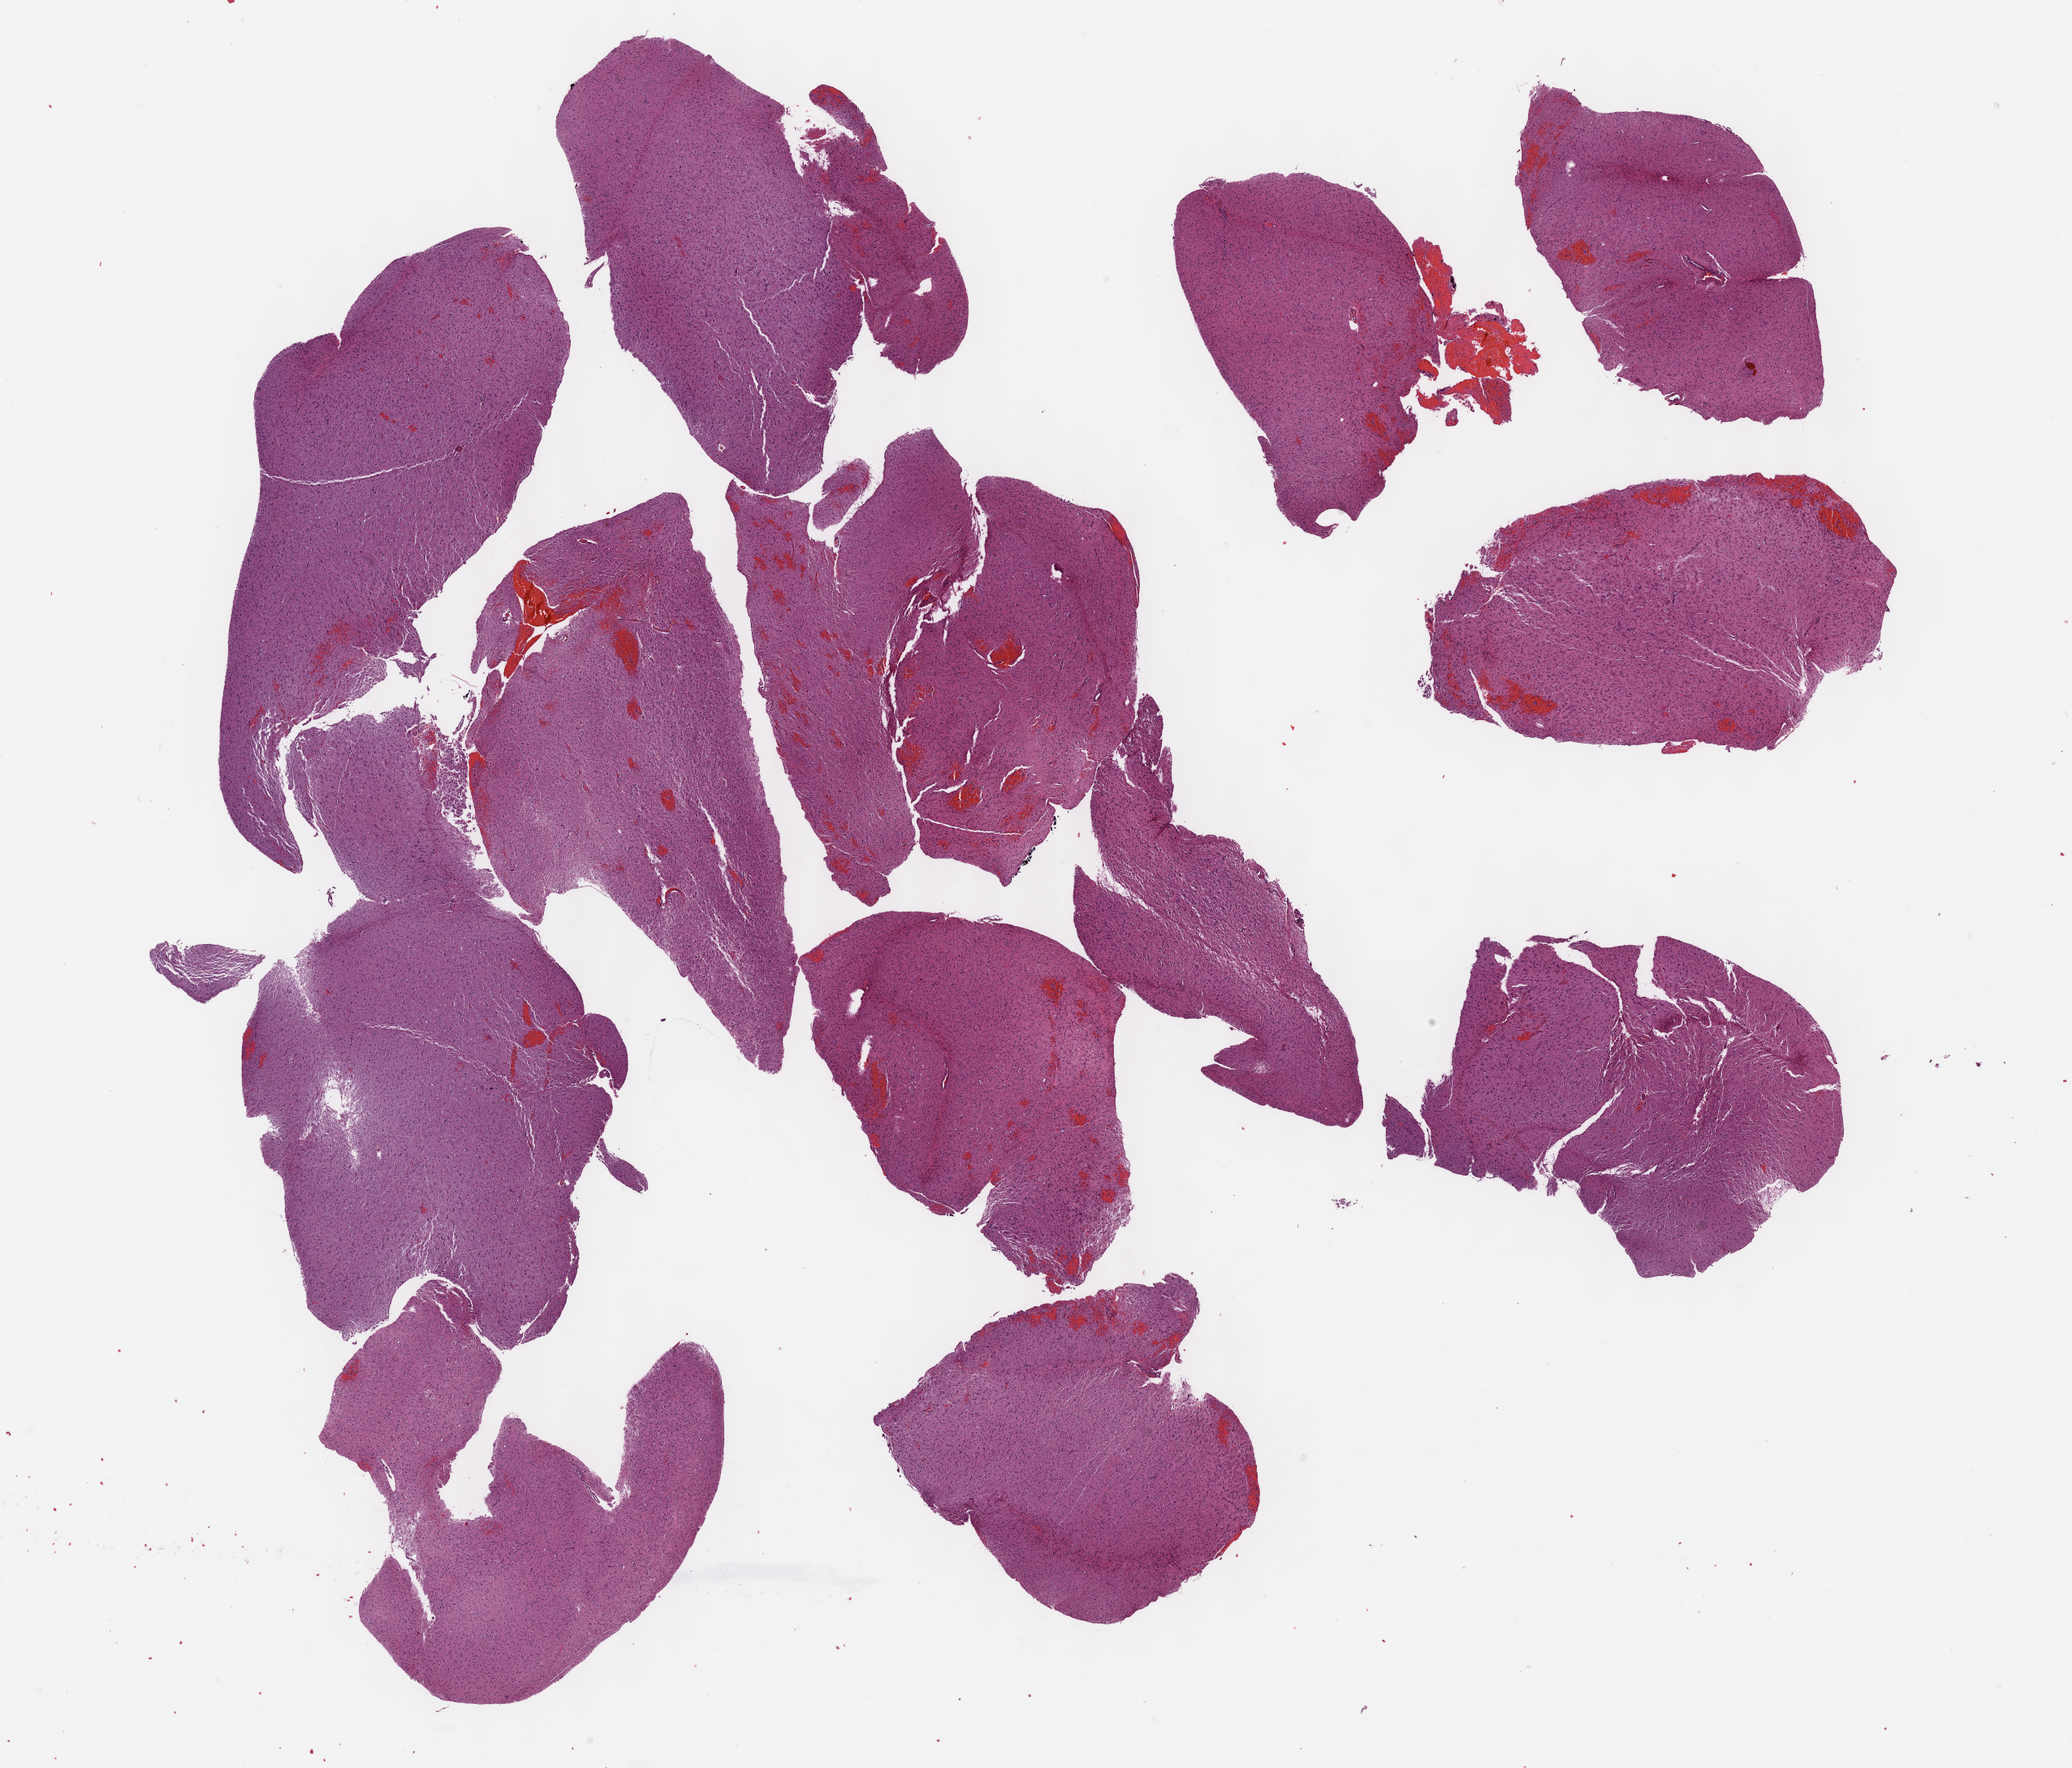
H&E-stained whole-slide image, whole scanned area (about 20.6 x 17.6 mm, slide scanned at 40x) shown as a low-resolution overview. FFPE section. Sample: primary tumour, brain. Patient: female, age at initial diagnosis 30 years. Histologic grade: G3 (poorly differentiated).
Histologic diagnosis: Astrocytoma, anaplastic. Laterality: left.